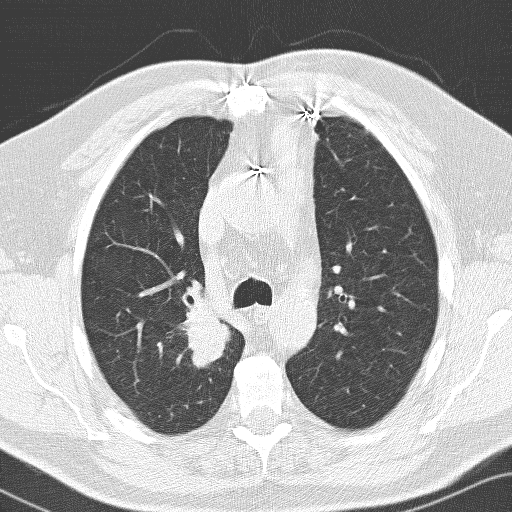
Low-dose screening chest CT, one axial slice; position 103 of 141 along the scan axis; 120 kVp; lung window (W 1500 / L -600 HU); 3.2 mm slice thickness; 512 × 512 image matrix.
Annotated regions visible in this slice (outlined manually by an expert reader):
- lesion 1 (tumor, upper lobe of right lung): bounding box (x1, y1, x2, y2) in pixels: (181, 302, 231, 368)